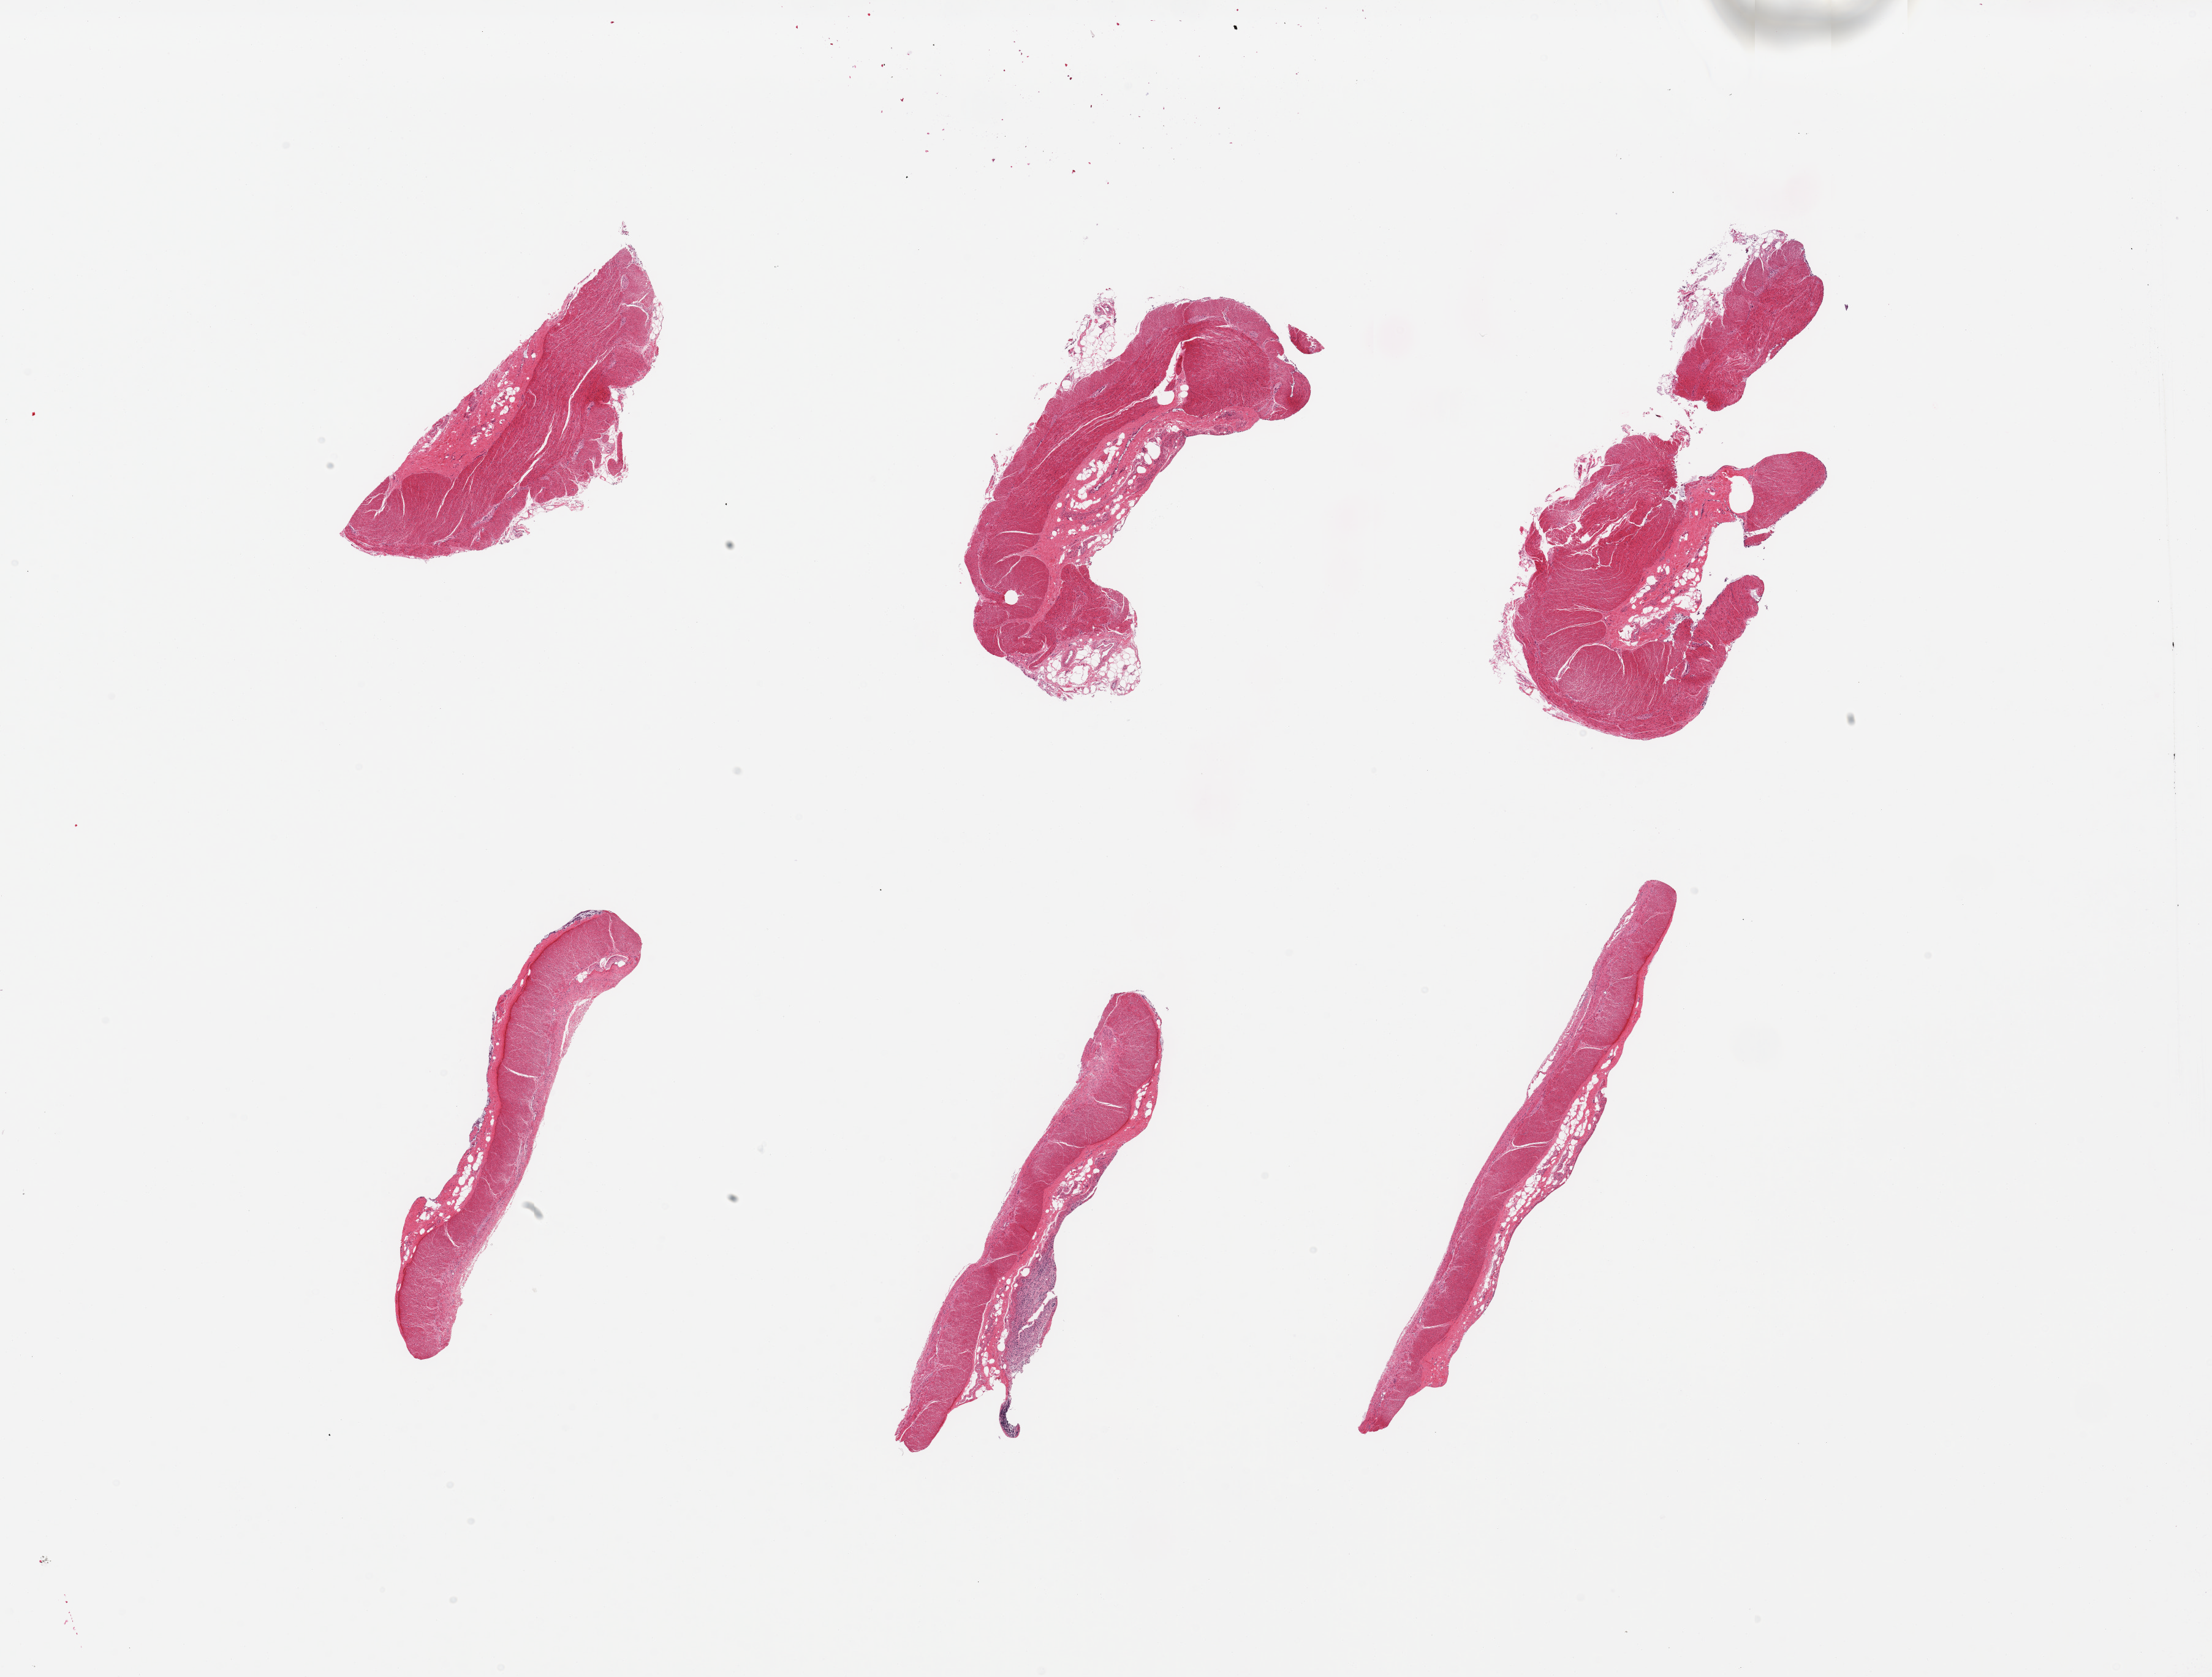
Hematoxylin and eosin (H&E) whole-slide image — a low-resolution overview of the entire scanned area, about 28.5 x 21.6 mm (acquisition: 20x scan), PAXgene-fixed paraffin-embedded (PFPE) section, sampled site (target tissue): sigmoid colon, donor tissue sample.
* pathologist's review note for this sample: 6 pieces, confirmed muscularis